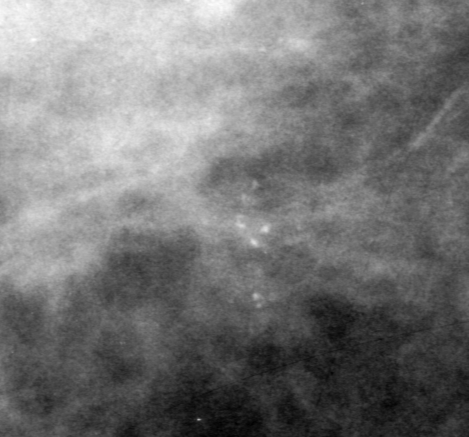
Region of interest cut from a scanned film mammogram (one marked finding), right breast, CC view.
Marked abnormality: calcifications, morphology pleomorphic, distribution clustered; BI-RADS assessment category 0 (incomplete: needs additional imaging); subtlety rating 4 on a 1 (subtle) to 5 (obvious) scale; pathology (as recorded): malignant.